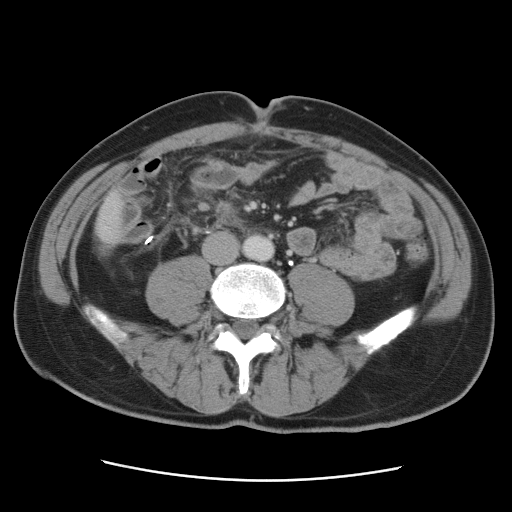
Contrast-enhanced abdominal CT, one axial slice; soft-tissue window (W 400 / L 40 HU); 512 × 512 image matrix, field of view 366 × 366 mm. Male patient, age 59 years. Case-level facts recorded for this patient, not image findings: diagnosis: colorectal cancer liver metastases, imaged before liver resection; multiple liver metastases: yes; largest metastasis: 0.6 cm.
Structures marked on this image (outlined manually by an expert reader):
- liver: bounding box [x1, y1, x2, y2] px = [96, 194, 123, 249]
- planned liver remnant (the part of the liver to remain after resection): [97, 195, 123, 250]